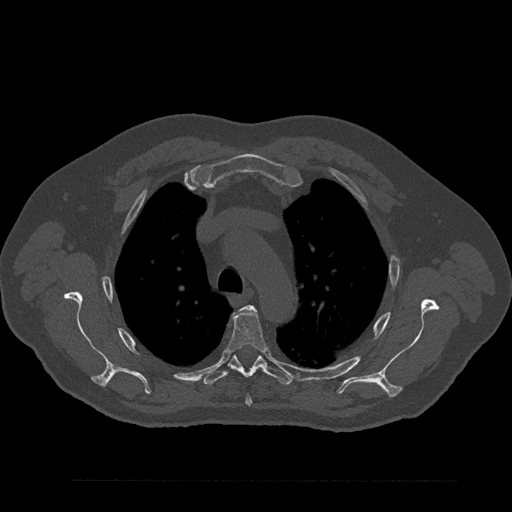
CT including the spine, one axial slice; position 628 of 797 along the scan axis; reconstruction kernel Br40s/3; 120 kVp; bone window (W 1800 / L 400 HU); 0.5 mm slice thickness; 512 × 512 image matrix, field of view 430 × 430 mm. Patient: male, 61 years. Case-level facts recorded for this patient, not image findings: primary cancer: prostate.
Structures marked on this image (semi-automatically segmented with operator editing):
- T3 vertebra: bounding box <243,306,255,310> (left, top, right, bottom; pixels)
- T4 vertebra: <227,307,268,406>
- T5 vertebra: <203,355,292,386>